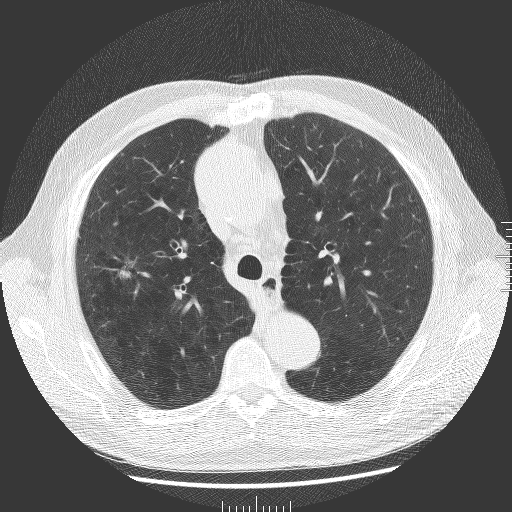
Low-dose screening chest CT, one axial slice; reconstruction kernel BONE; lung window (W 1500 / L -600 HU); 2 mm slice thickness; 512 × 512 image matrix, field of view 380 × 380 mm.
Outlined on this slice (outlined manually by an expert reader):
- lesion 1 (tumor, upper lobe of right lung): bounding box <120,270,130,278> (left, top, right, bottom; pixels)